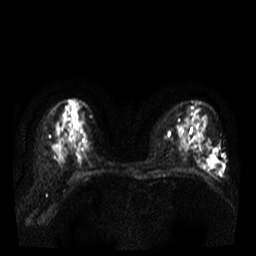
Breast MRI, one axial slice; slice 22 of 38 in the series (ordered by position); diffusion-weighted series; image 2 of 4 stored at this slice position (different b-values; order by instance number); 3 T; 5 mm slice thickness; 256 × 256 image matrix, field of view 320 × 320 mm. Female patient.
Annotated regions visible in this slice (outlined manually by an expert reader):
- tumour on diffusion-weighted imaging: box from (x=208, y=156) to (x=218, y=168) px